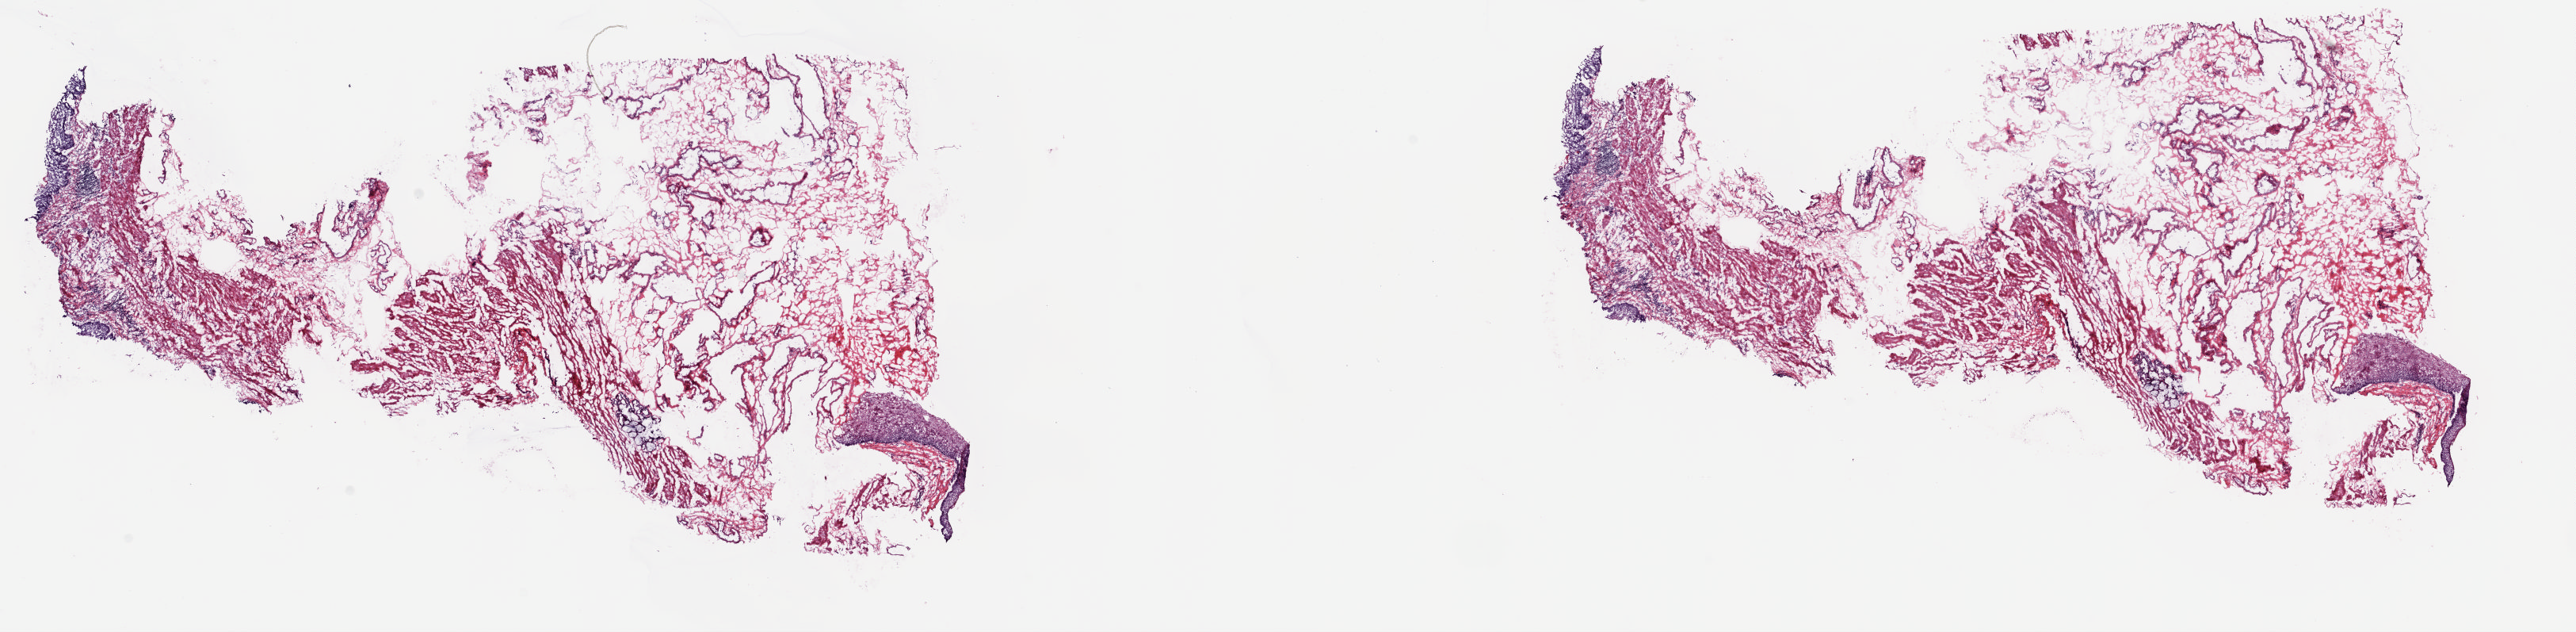
Hematoxylin and eosin (H&E) stained whole-slide image, a low-resolution overview of the entire scanned area, about 25.8 x 6.3 mm (slide scanned at 20x), frozen section from the top of the tissue portion, esophagus, solid tissue normal (non-tumour tissue) sample. Female patient; age at initial diagnosis 69 years. Composition of this section per pathologist review: tumour cells 0%, tumour nuclei 0%.
This section: solid tissue normal sample (biorepository sample class). Patient diagnosis: Squamous cell carcinoma, NOS.